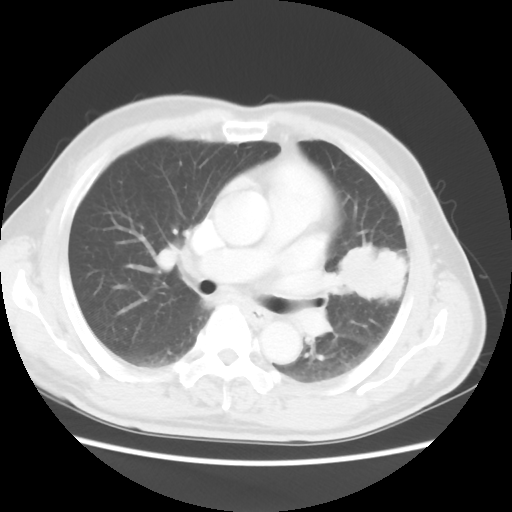
Chest CT, one axial slice. Position 29 of 50 along the scan axis. Reconstruction kernel STANDARD. Lung window (W 1500 / L -600 HU). 5 mm slice thickness. 512 × 512 image matrix, field of view 360 × 360 mm. Male patient, age 69 years. Case-level facts recorded for this patient, not image findings: clinical TNM (as recorded): T3 N1 M1a.
Annotated regions visible in this slice (bounding box drawn by a radiologist):
- lung tumour (recorded histology: squamous cell carcinoma): bounding box [x1, y1, x2, y2] px = [337, 234, 416, 323]